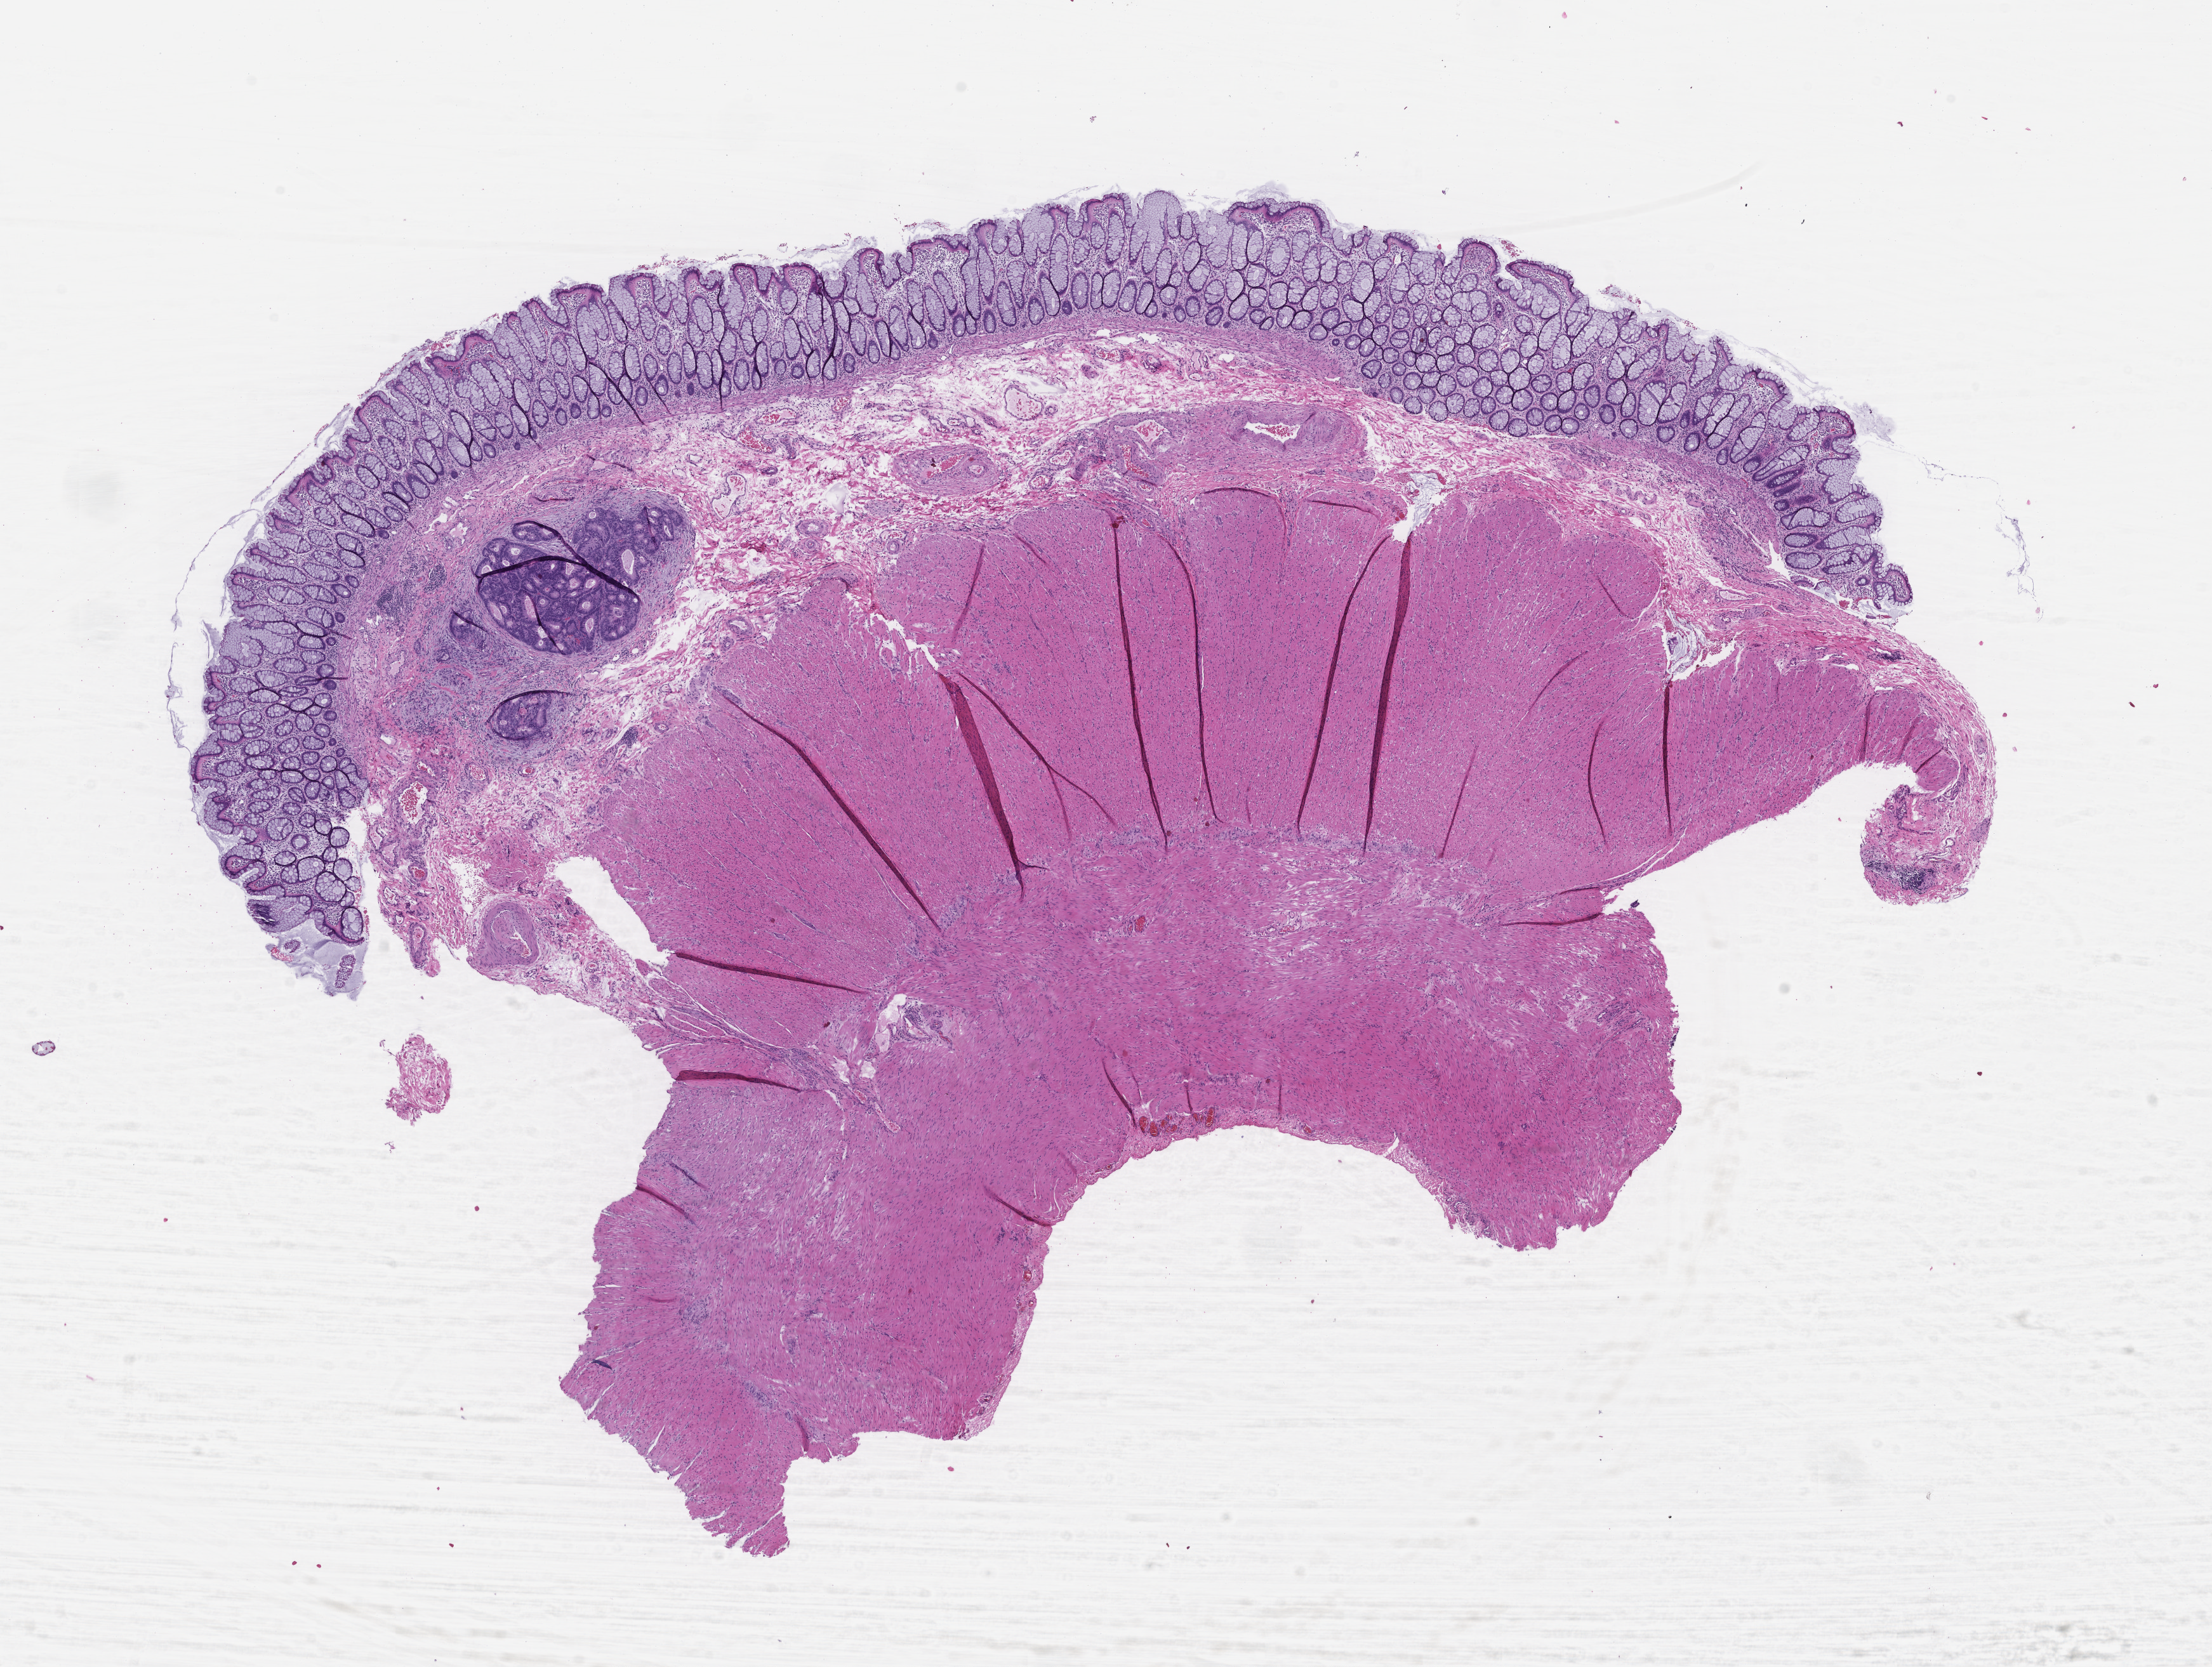
Hematoxylin and eosin (H&E) whole-slide image — a low-resolution overview of the entire scanned area, about 14.1 x 10.6 mm; formalin-fixed paraffin-embedded section; tissue site: colon; specimen time point: collected on treatment. Female patient.
* this section: primary tumor
* diagnosis: Colorectal Carcinoma